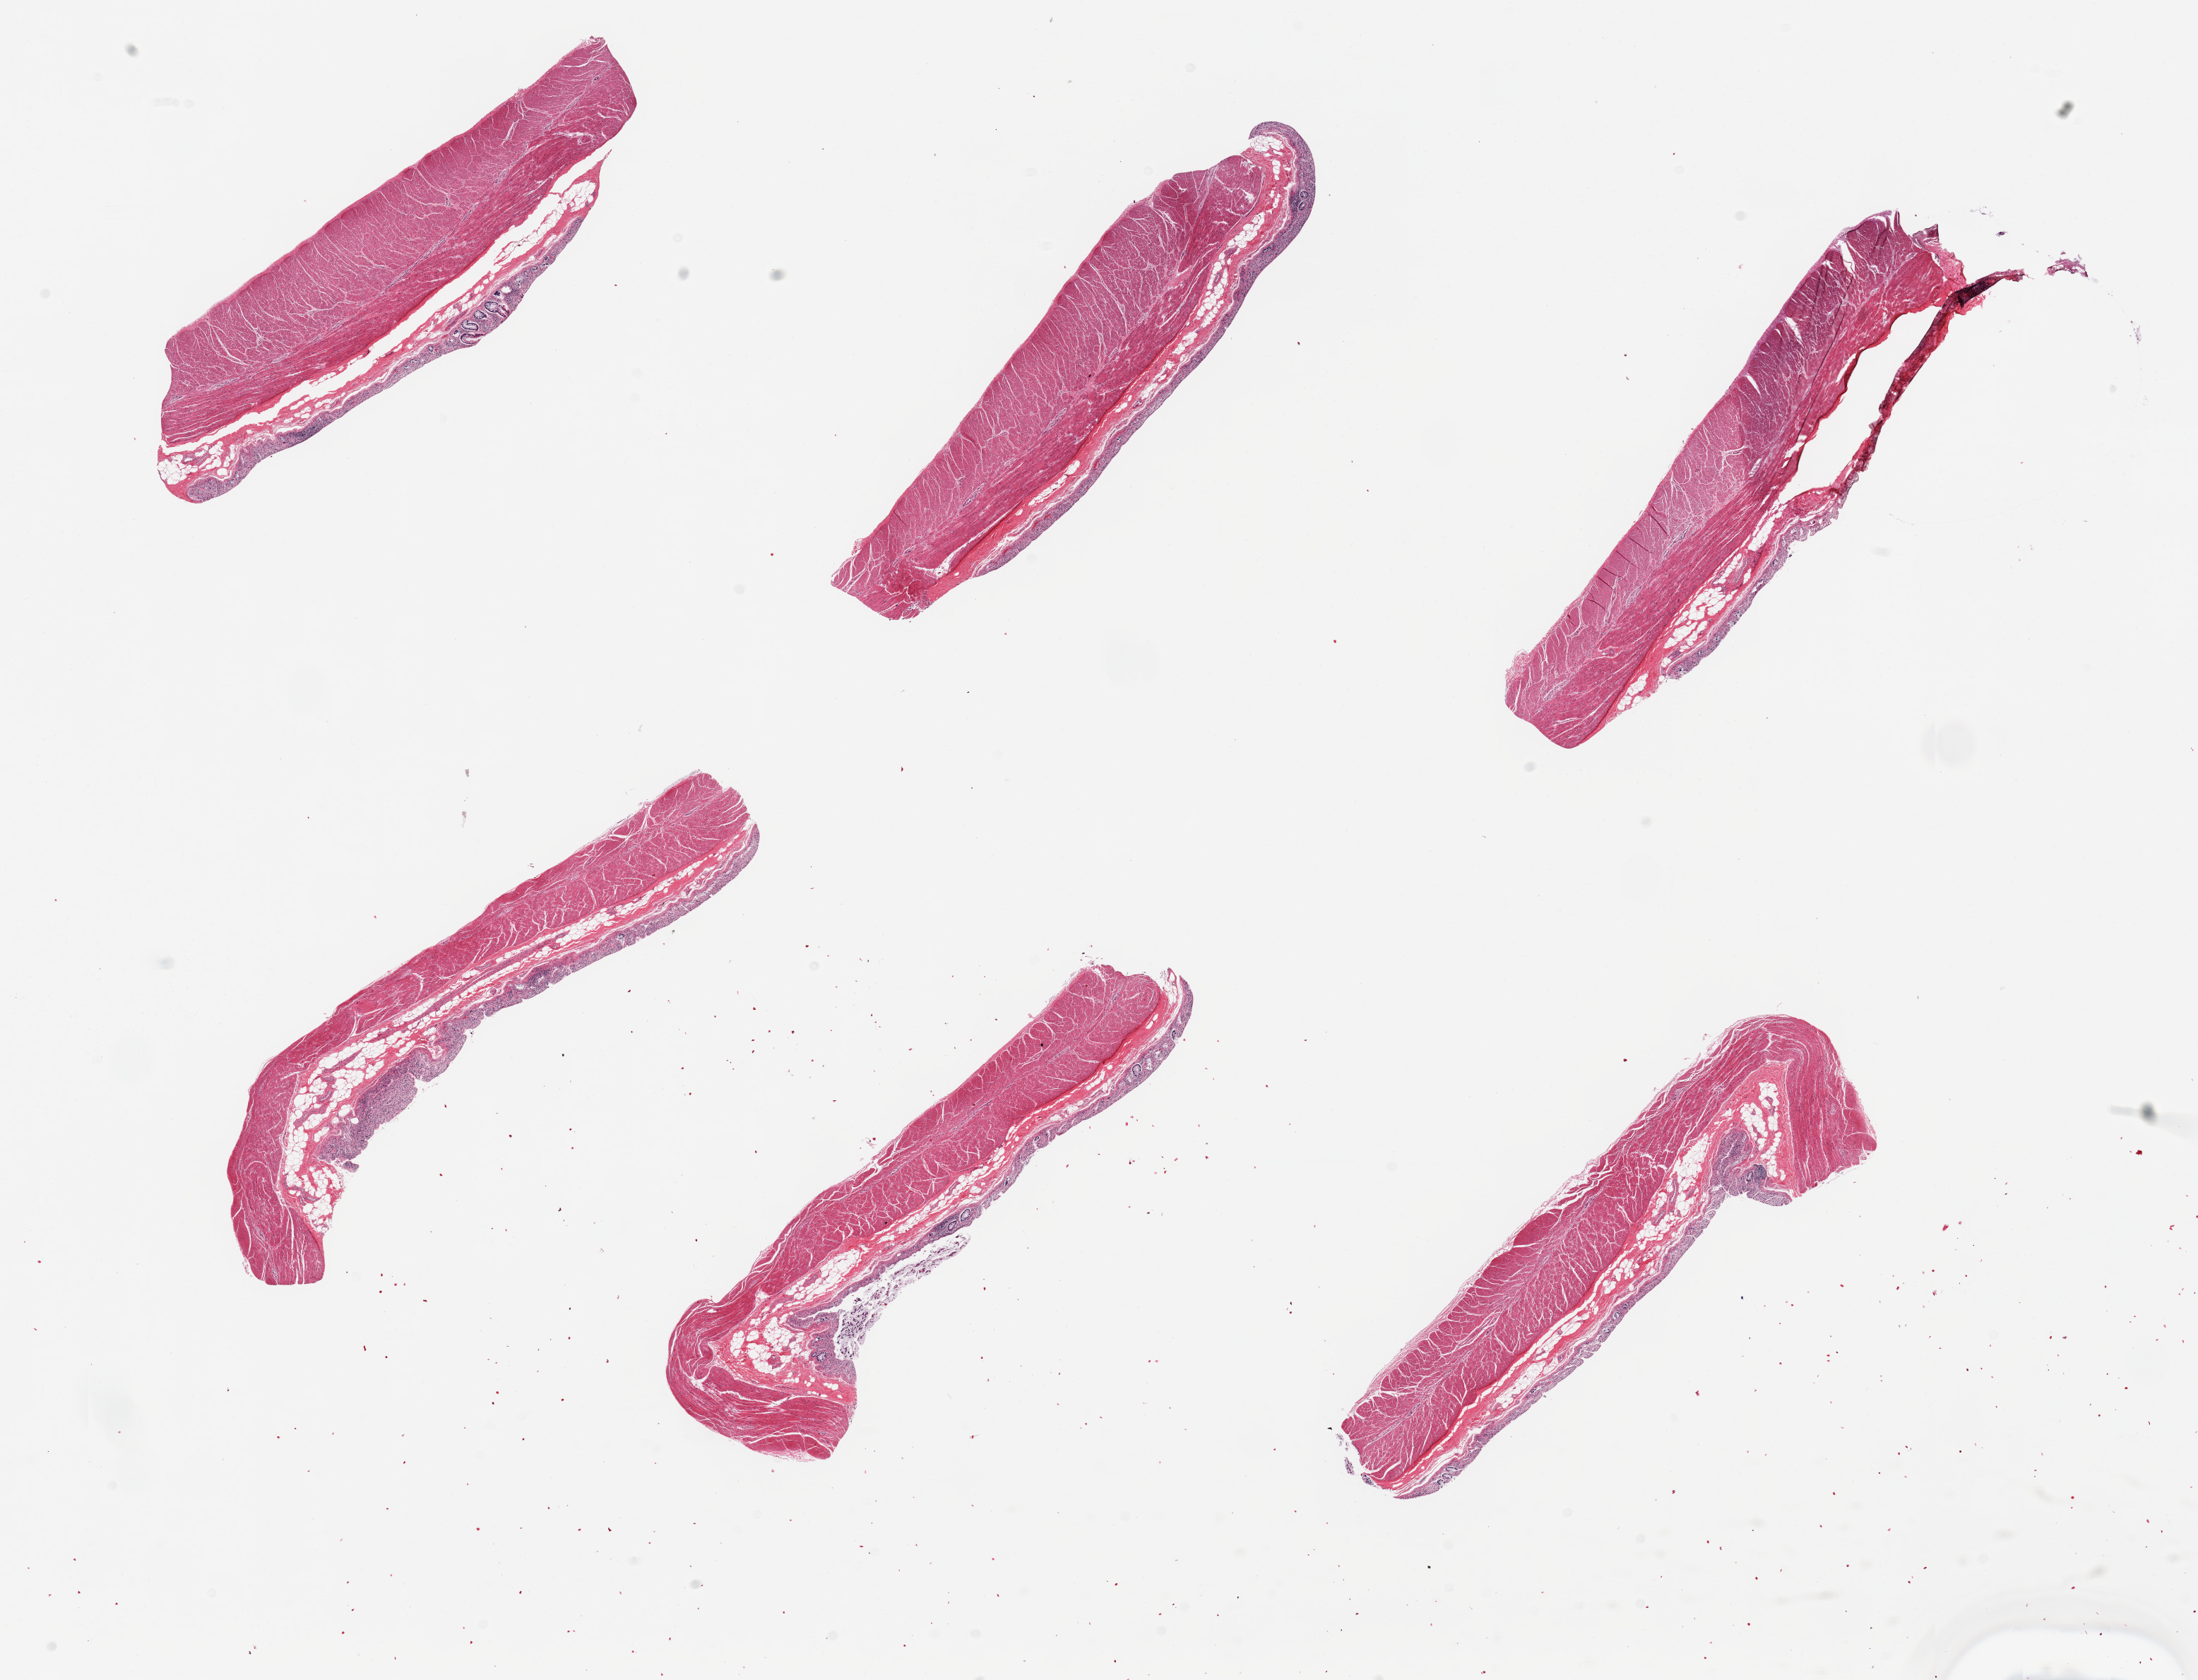
H&E whole-slide image, brightfield — a low-resolution overview of the entire scanned area, about 24.6 x 18.8 mm; PAXgene-fixed paraffin-embedded (PFPE) section; sampled site (target tissue): sigmoid colon; donor tissue sample.
Review note (as recorded): 6 pieces; all are full thickness (target is muscularis).